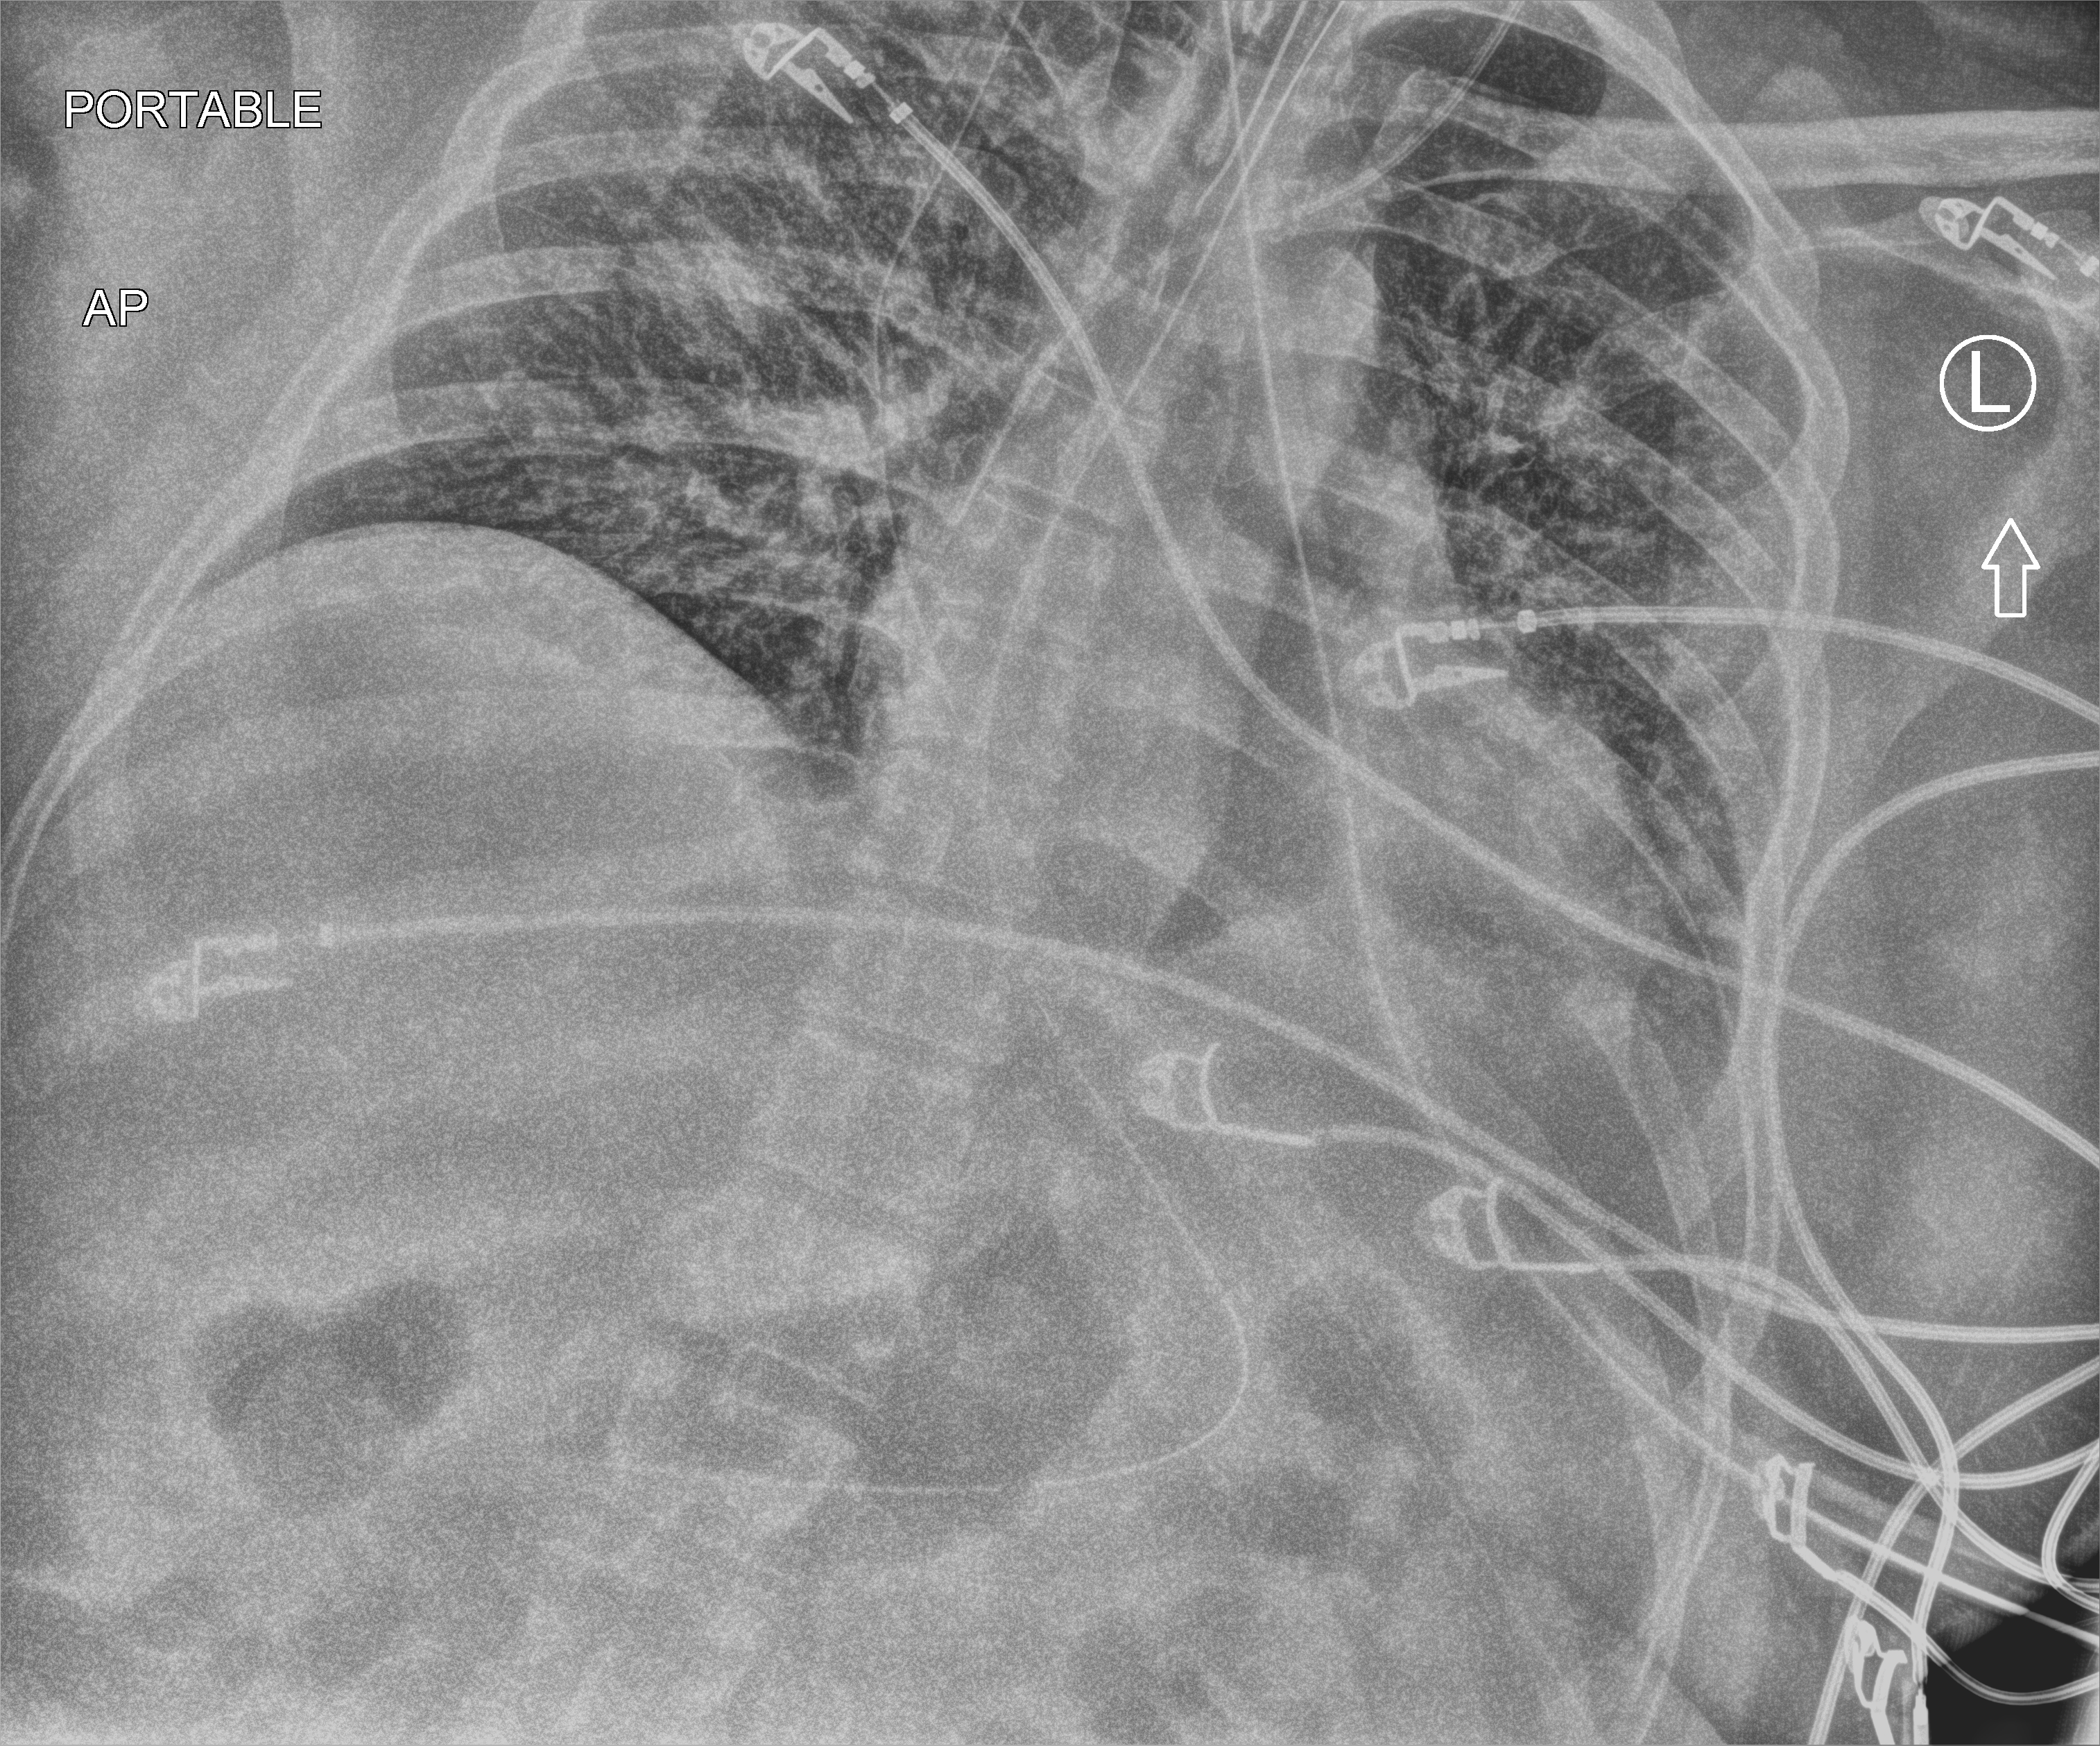
Chest X-ray (portable), anteroposterior (AP) projection. Adult patient hospitalised with COVID-19, age 18–59 years.
From the hospital-stay record, not from the radiograph (when in the stay this image was taken is not recorded): length of hospital stay: 16 days.